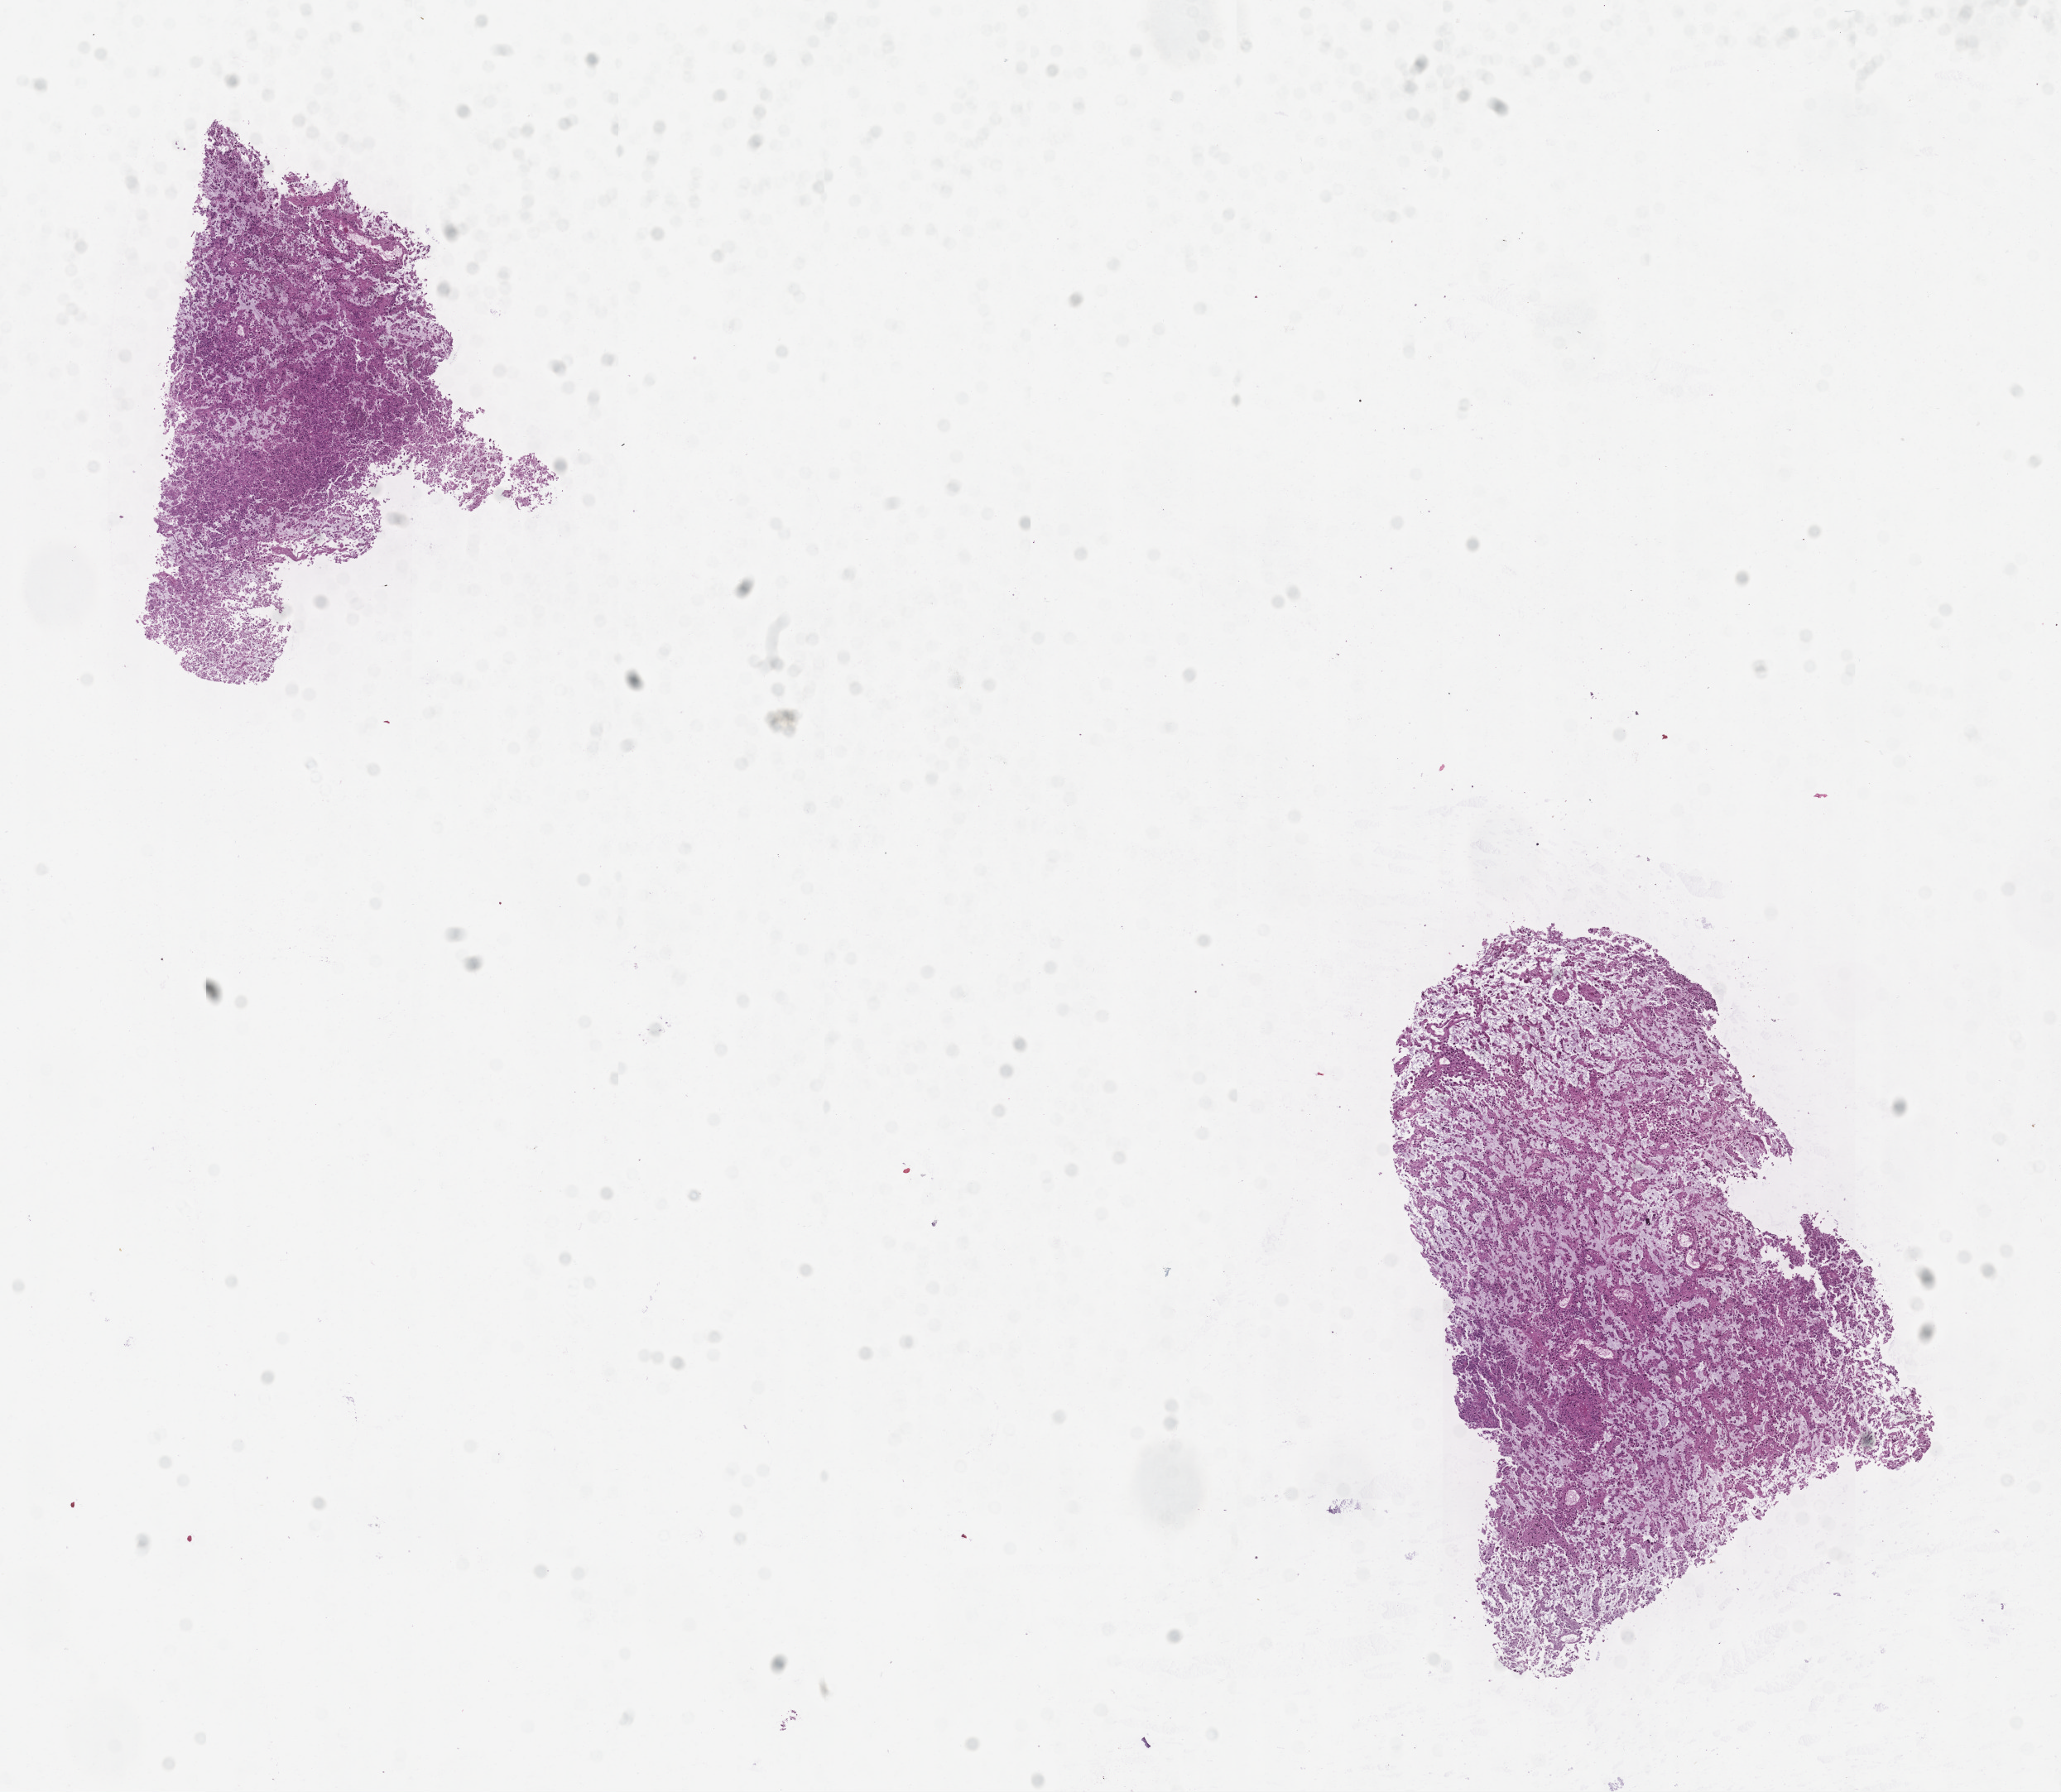
H&E whole-slide image — shown as a low-resolution overview of the whole scanned area (about 10.0 x 8.7 mm, acquisition: 20x scan); brain, tumour tissue. Male, 35 y/o.
Diagnosis: Glioblastoma.